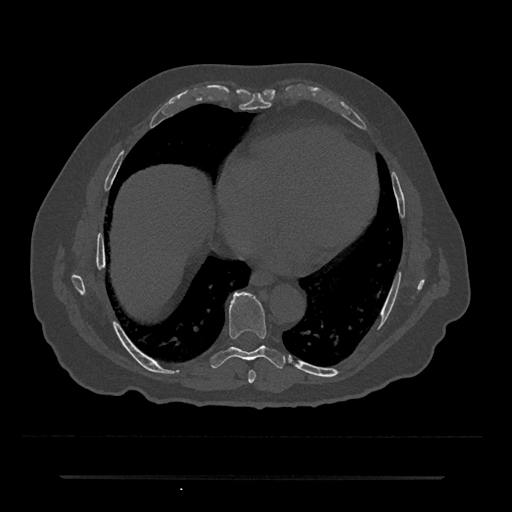
CT including the spine, one axial slice; slice 334 of 797 in the series (ordered by position); 120 kVp; bone window (W 1800 / L 400 HU); 0.5 mm slice thickness; 512 × 512 image matrix, field of view 437 × 437 mm. Patient: male, 69 years. From the clinical record (not read from this slice): primary cancer: prostate.
Annotated regions visible in this slice (semi-automatically segmented with operator editing):
- T7 vertebra: bounding box [x1, y1, x2, y2] px = [248, 370, 256, 383]
- T8 vertebra: [211, 292, 285, 369]